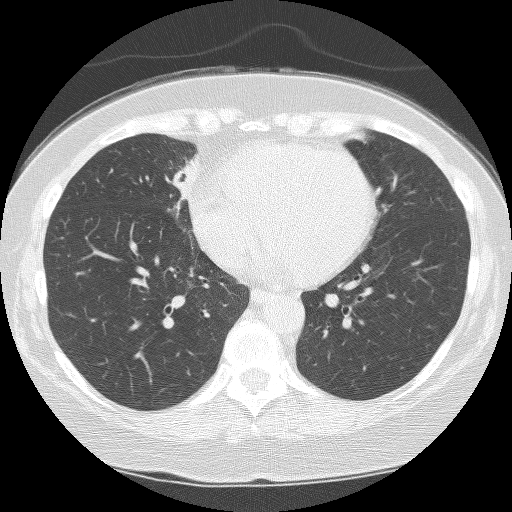
Low-dose screening chest CT, one axial slice. Slice 72 of 159 in the series (ordered by position). Reconstruction kernel BONE. Lung window (W 1500 / L -600 HU). 2.5 mm slice thickness. 512 × 512 image matrix.
Annotated regions visible in this slice (expert manual segmentation):
- lesion 1 (tumor, hilum of right lung): bounding box <172,154,198,201> (left, top, right, bottom; pixels)